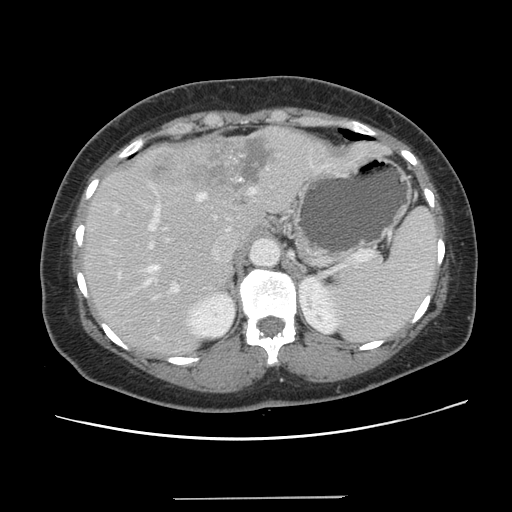
Contrast-enhanced abdominal CT, one axial slice; slice 93 of 141 in the series (ordered by position); intravenous contrast given; soft-tissue window (W 400 / L 40 HU); 2.5 mm slice thickness; 512 × 512 image matrix, field of view 366 × 366 mm. Female patient, age 53 years. Case-level facts recorded for this patient, not image findings: diagnosis: colorectal cancer liver metastases, imaged before liver resection.
Annotated regions visible in this slice (expert manual segmentation):
- hepatic veins: bounding box <144,193,234,285> (left, top, right, bottom; pixels)
- liver: <84,128,386,354>
- planned liver remnant (the part of the liver to remain after resection): <84,209,263,355>
- portal vein (with intrahepatic branches): <148,188,255,300>
- liver metastasis: <145,138,271,200>